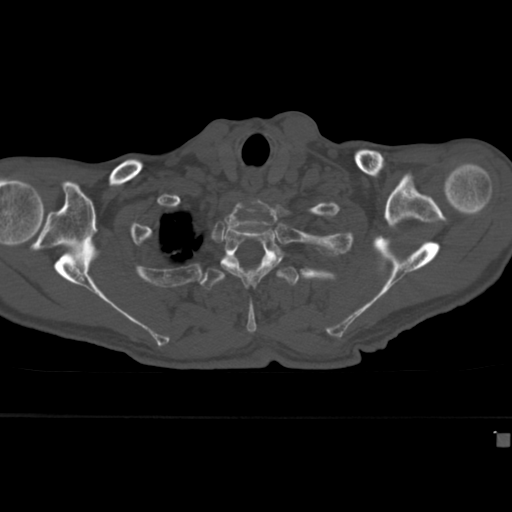
CT including the spine, one axial slice; position 342 of 430 along the scan axis; reconstruction kernel Br40s; 120 kVp; bone window (W 1800 / L 400 HU); 1.5 mm slice thickness; 512 × 512 image matrix, field of view 337 × 337 mm. Patient: male, 64 years. Case-level facts recorded for this patient, not image findings: primary cancer: uterus; vertebrae with lytic lesions (as recorded): T1, T4, T5, T7, L5.
Annotated regions visible in this slice (semi-automatically segmented with operator editing):
- T2 vertebra: bounding box [x1, y1, x2, y2] px = [220, 223, 283, 289]
- T3 vertebra: [199, 259, 299, 334]